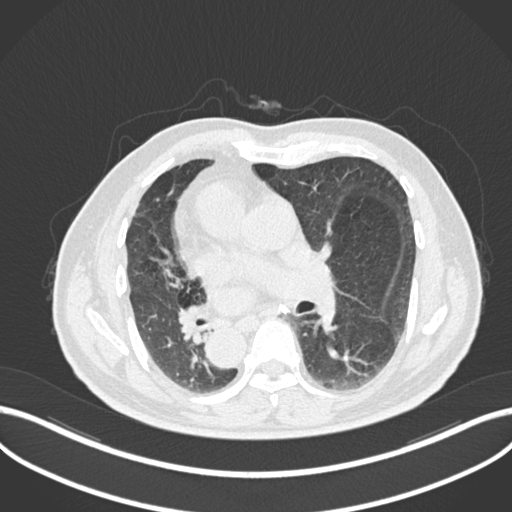
Chest CT, one axial slice. Reconstruction kernel B30f. Lung window (W 1500 / L -600 HU). 512 × 512 image matrix, field of view 400 × 400 mm. Patient: male, 67 years. Case-level facts recorded for this patient, not image findings: clinical TNM (as recorded): T2a N0 M0.
Annotated regions visible in this slice (bounding box drawn by a radiologist):
- lung tumour (recorded histology: squamous cell carcinoma): box from (x=176, y=302) to (x=212, y=344) px